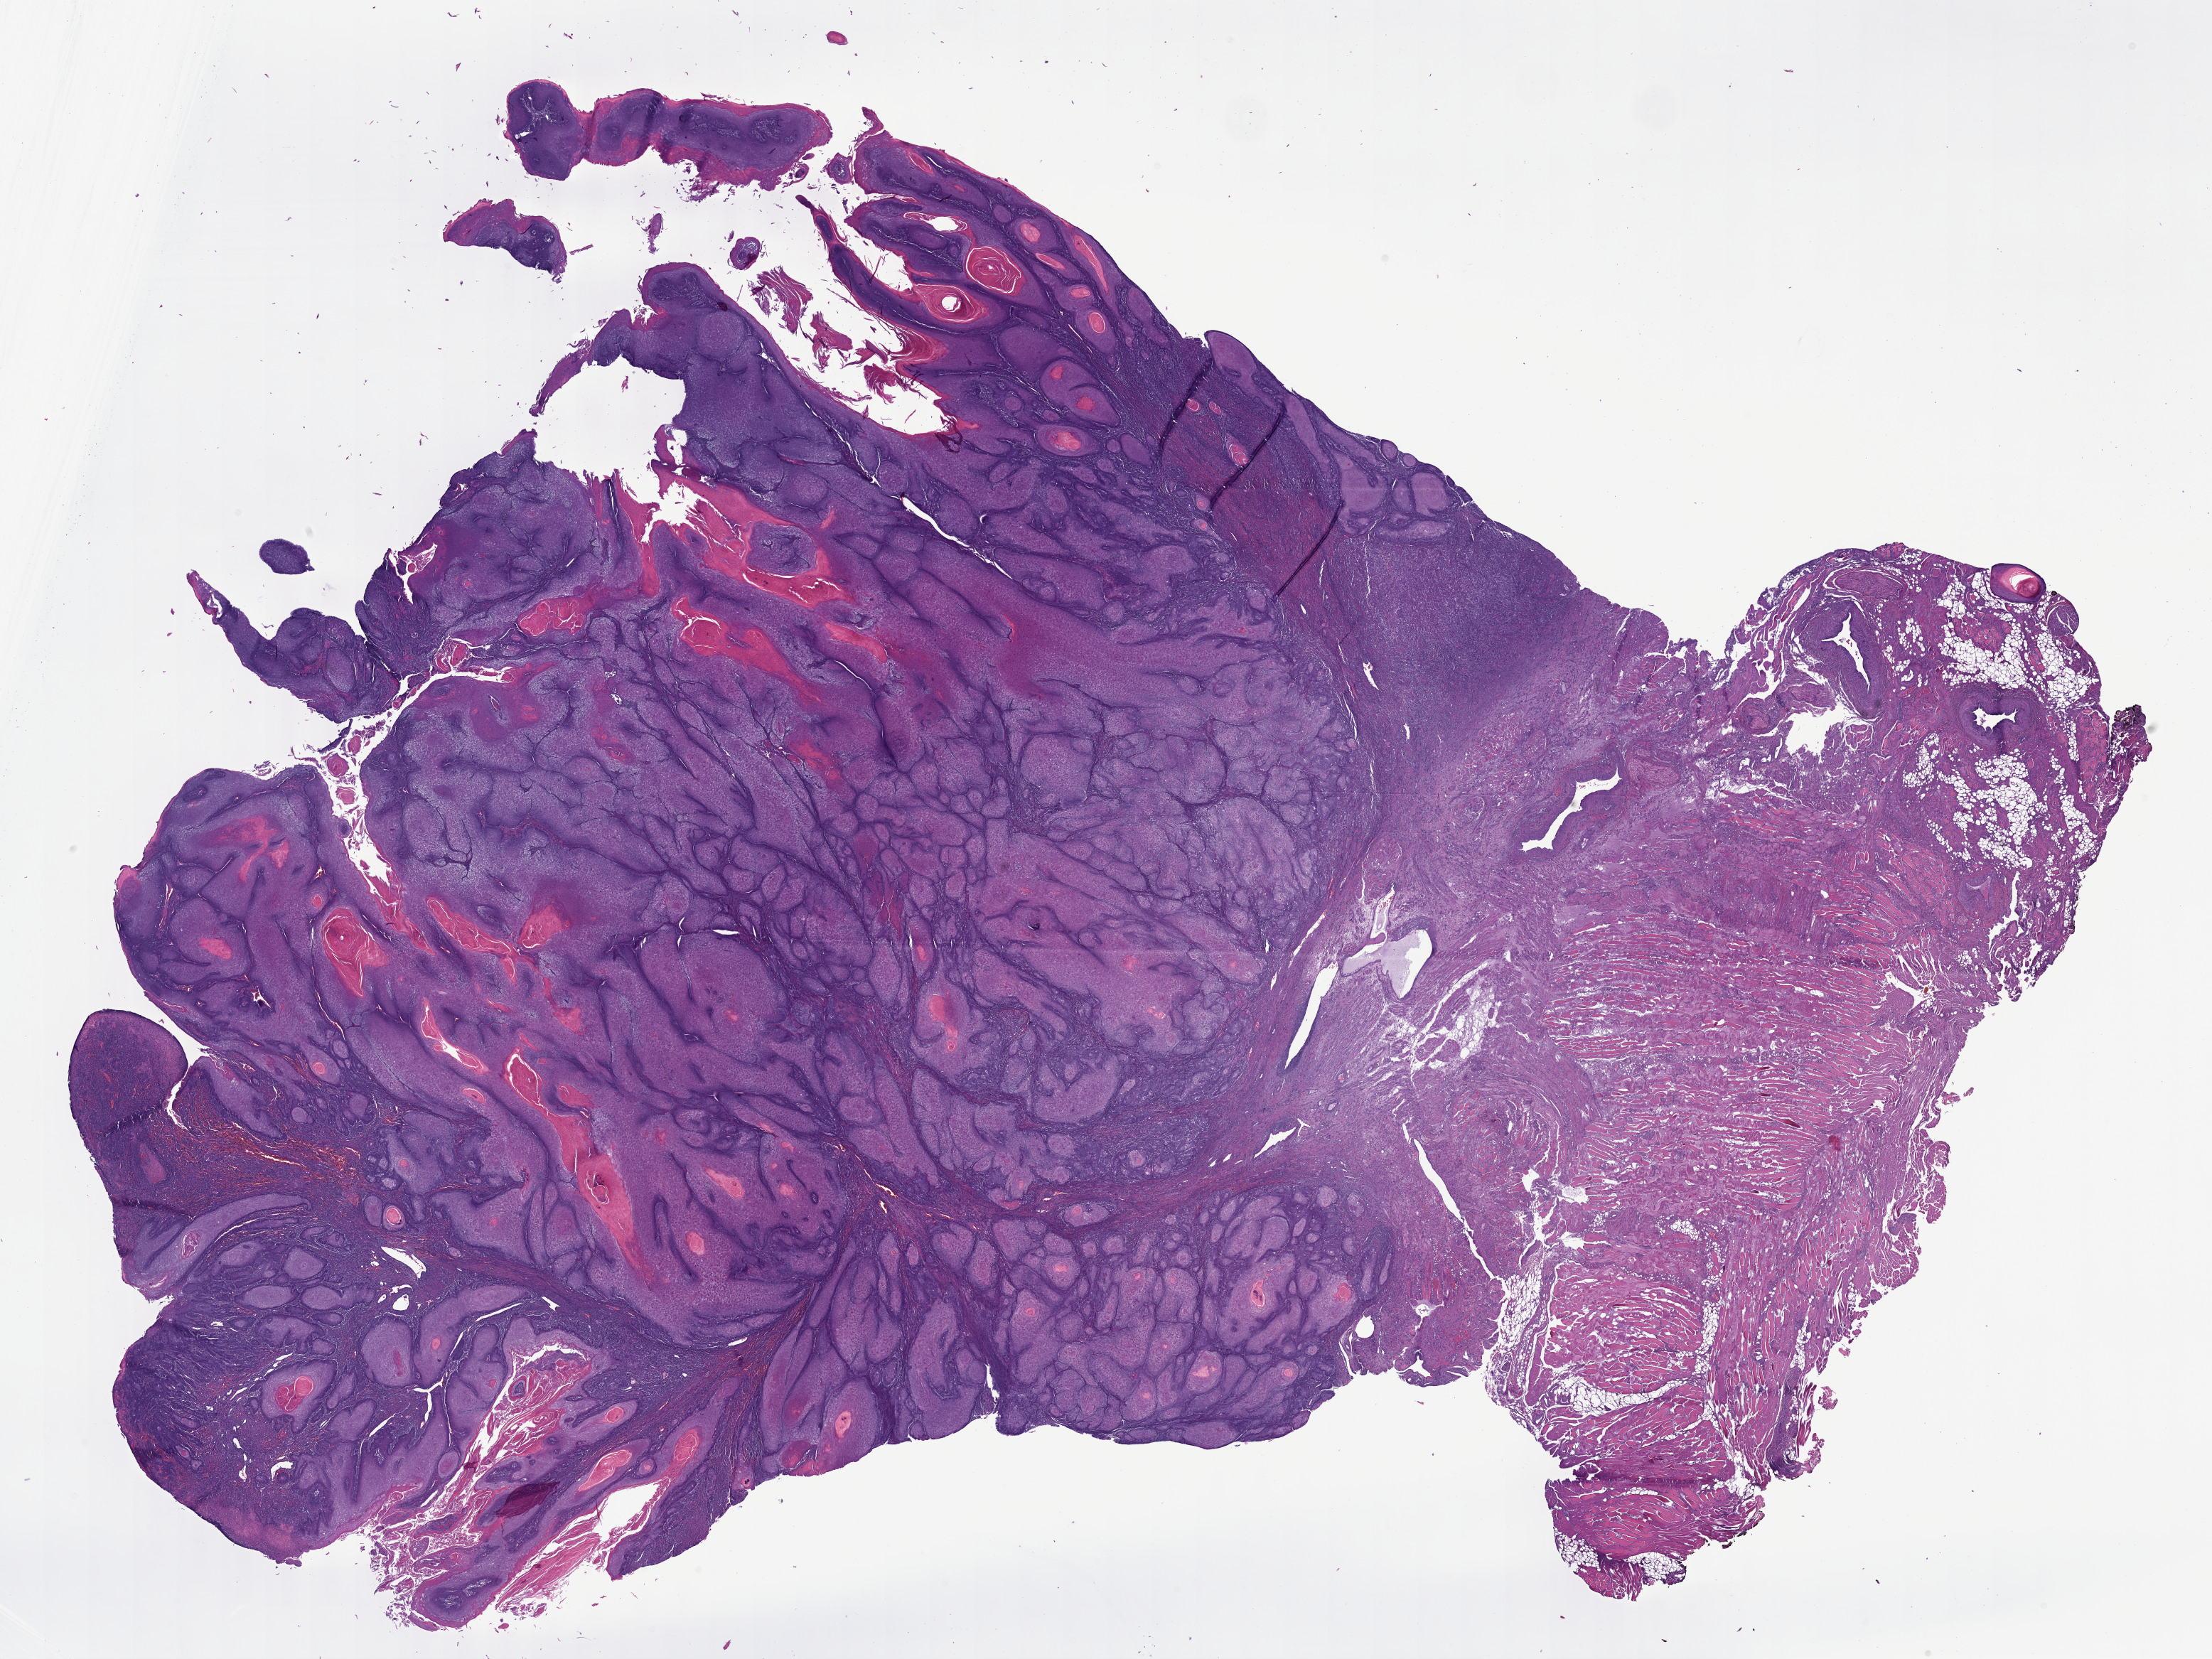
Hematoxylin and eosin (H&E) stained whole-slide image, shown as a low-resolution overview of the whole scanned area (about 25.1 x 18.9 mm, from a 40x scan); formalin-fixed paraffin-embedded (FFPE) diagnostic section; sample: primary tumour, head and neck. Male patient; age at initial diagnosis 62 years. Histologic grade: G1 (well differentiated).
TNM: T4a N0. Histologic diagnosis: Squamous cell carcinoma, NOS (tongue, NOS). AJCC pathologic stage: IVA.